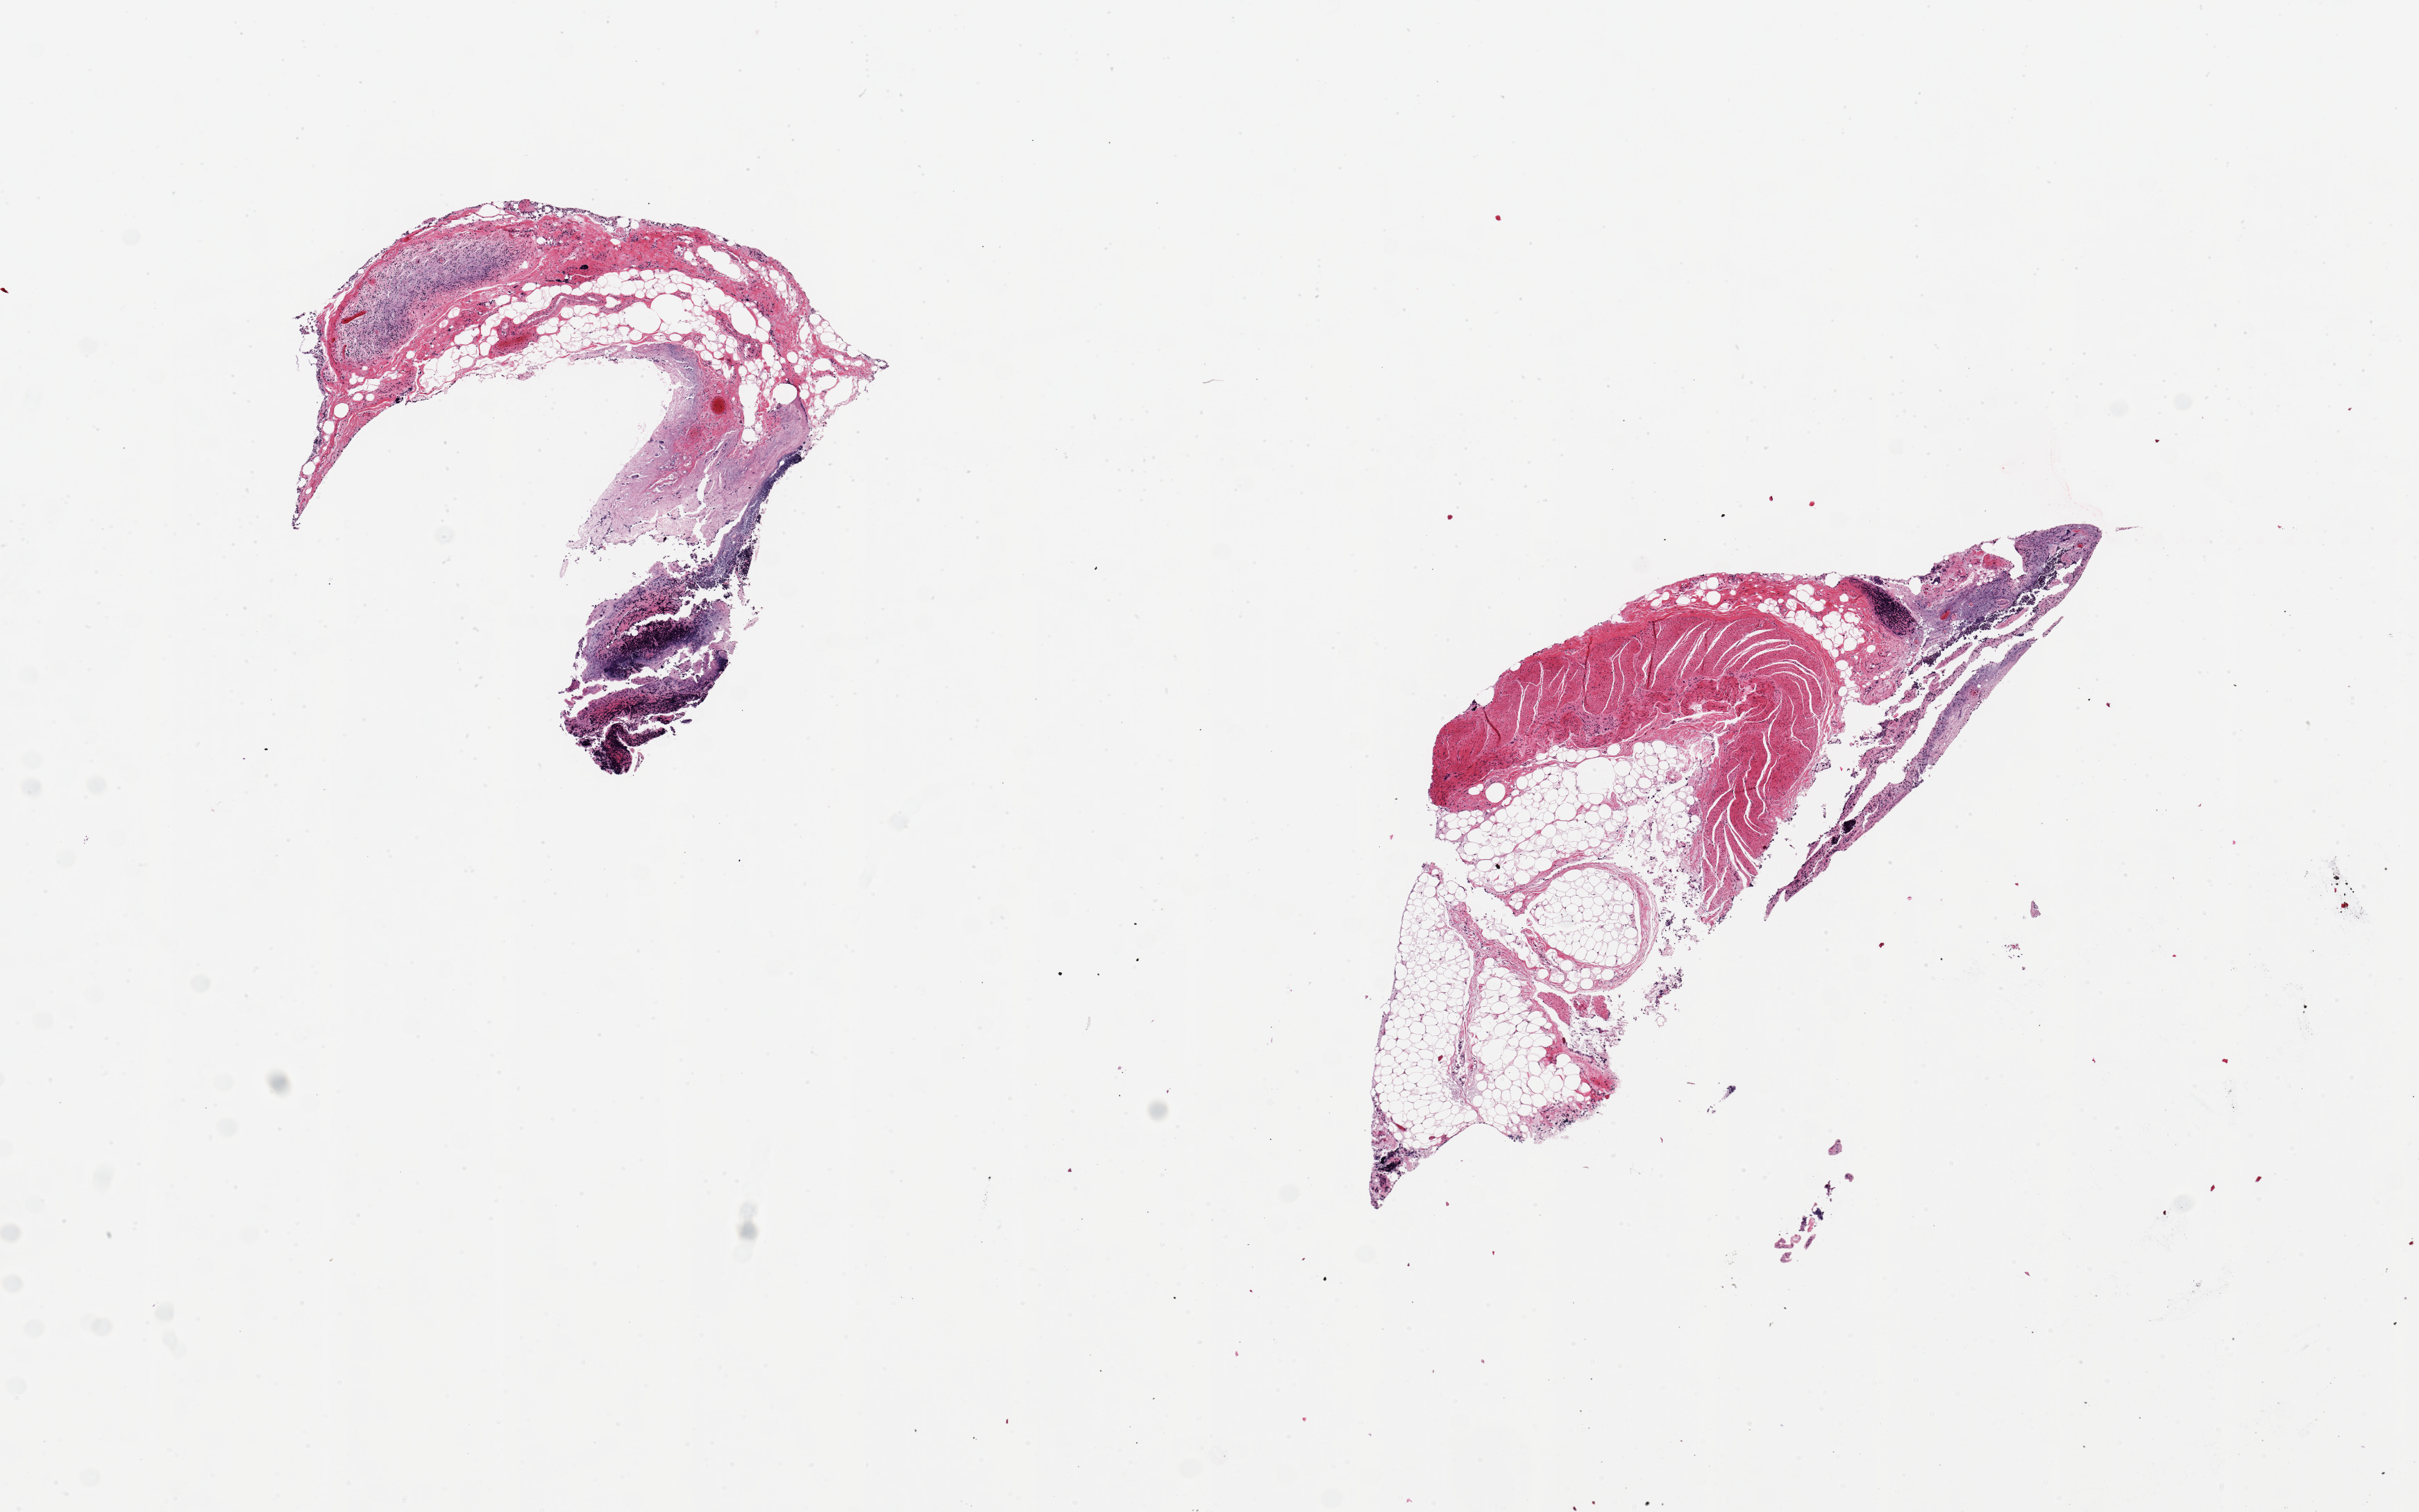
Whole-slide image, H&E stain — a low-resolution overview of the entire scanned area, about 13.8 x 8.6 mm; PAXgene-fixed paraffin-embedded (PFPE) section; section of ileum (target tissue); tissue donor sample. Donor: male.
Pathologist's review note for this sample: 2 pieces ~4x3mm, <10% lymphoid elements; badly autolyzed.